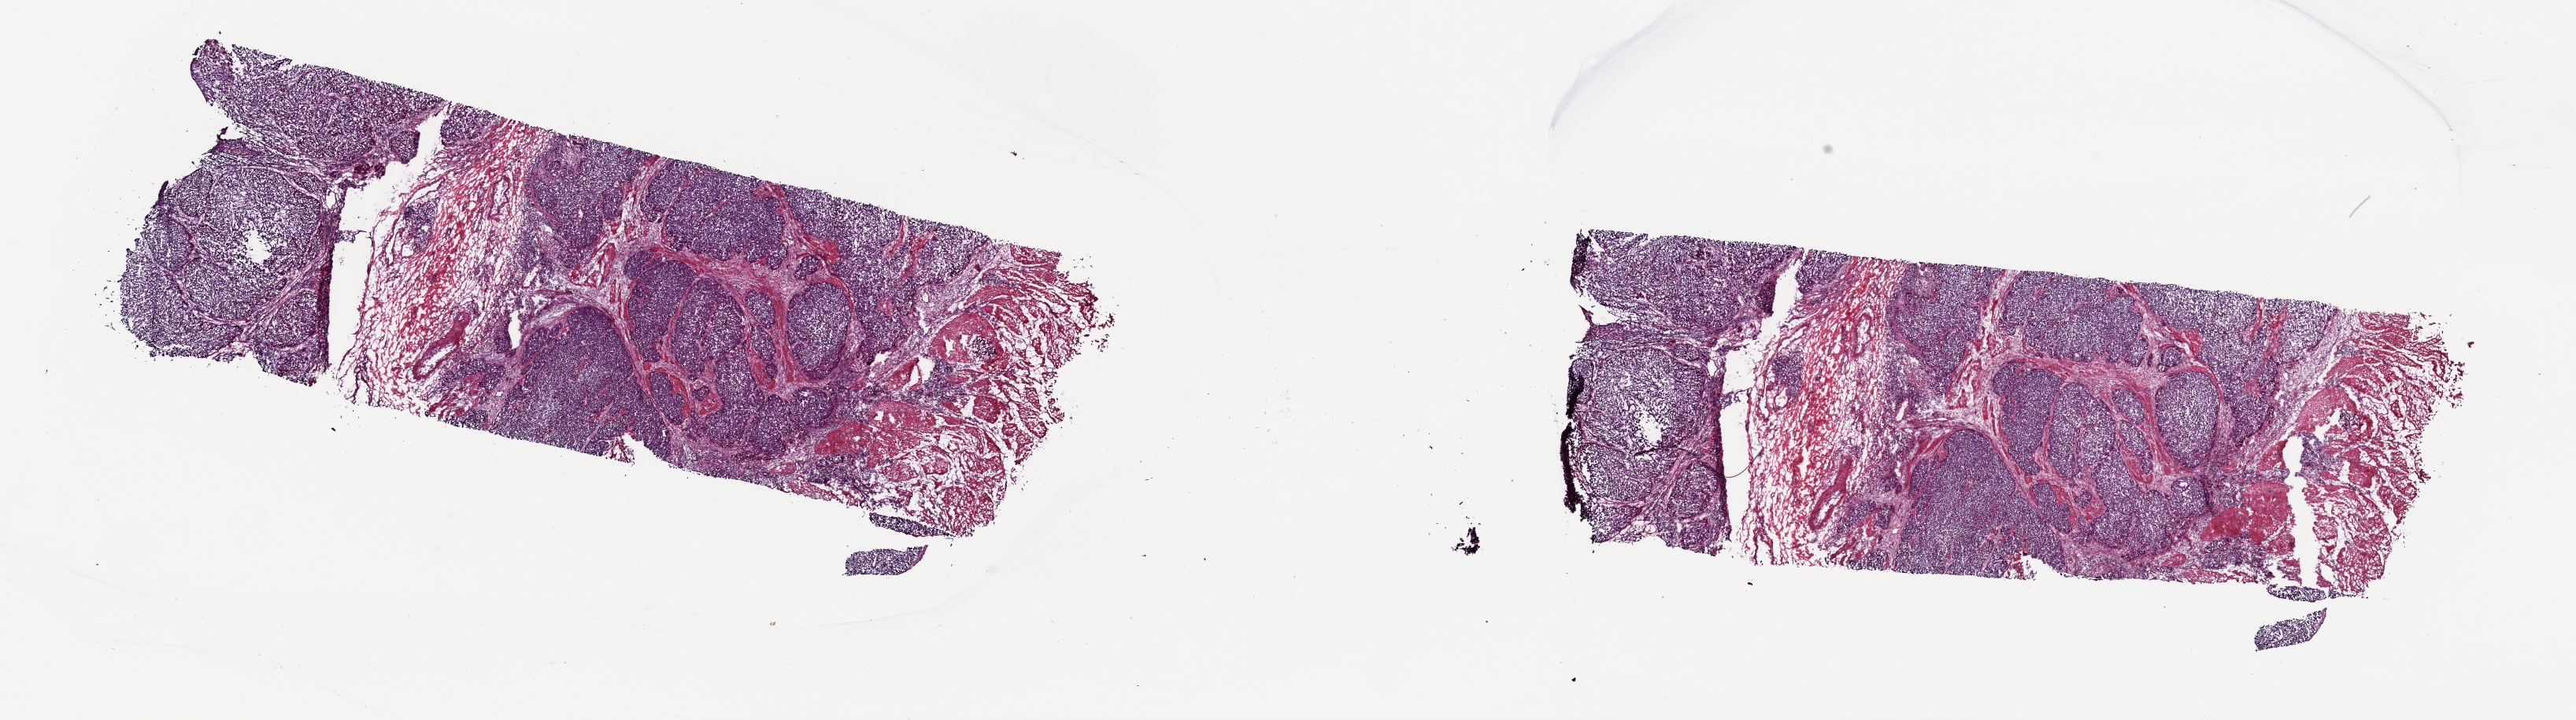
H&E whole-slide image, shown as a low-resolution overview of the whole scanned area (about 25.8 x 7.2 mm, slide scanned at 40x); frozen section from the top of the tissue portion; primary tumour sample from the esophagus. Male patient; age at initial diagnosis 57 years. Histologic grade: G2 (moderately differentiated). Pathologist review of this section (percent, as recorded): tumour cells 70%, tumour nuclei 90%, normal cells 10%, stromal cells 20%, necrosis 0%. Infiltration values recorded for this section: lymphocyte infiltration 6%, monocyte infiltration 2%, neutrophil infiltration 1%.
Lymph nodes positive (case pathology): 5 of 8 examined. AJCC pathologic stage: IV. TNM: T3 N1 M1. Diagnosis: Squamous cell carcinoma, NOS (lower third of esophagus).